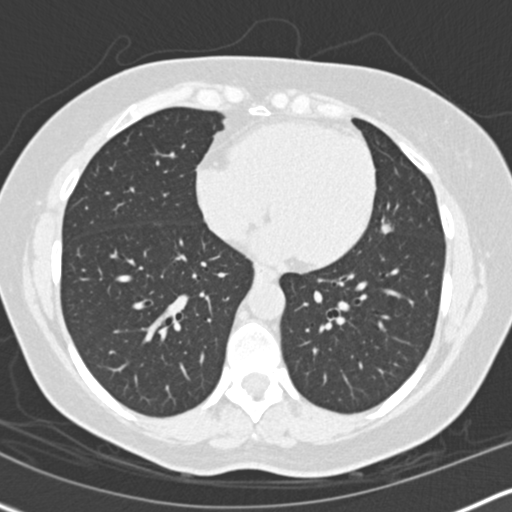
Low-dose screening chest CT, axial slice. Second screening round (one year after baseline). Lung window (W 1500 / L -600 HU). 2 mm slice thickness. Standard (soft-tissue) reconstruction kernel (B30f). Slice 94 of 158 in the series. 512 × 512 image matrix, field of view 310 × 310 mm. Female participant, aged 56 years at enrolment. Former smoker at enrolment.
• Expert reader's lesion annotation, bounding box (x1, y1, x2, y2) in pixels: (361, 201, 408, 248).
• Reader record for this screening exam (exam-level; its link to the box is not recorded): non-calcified nodule or mass ≥4 mm, lingula, 10 × 8 mm, smooth margins, soft tissue attenuation, pre-existing on the prior screen: yes; interval growth: yes.
• Official screen result: positive, other.
• Participant outcome: lung cancer diagnosed 506 days after this screen — adenocarcinoma, NOS, left upper lobe, poorly differentiated (G3), stage IIIA (AJCC 6th edition), 15 mm at pathology.